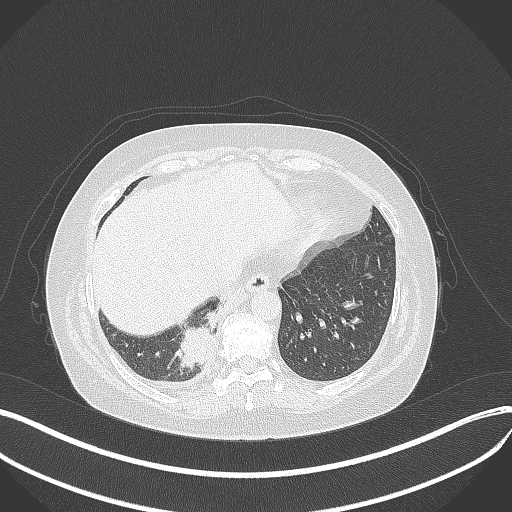
Chest CT, one axial slice; slice 92 of 381 in the series (ordered by position); reconstruction kernel B70f; lung window (W 1500 / L -600 HU); 1 mm slice thickness; 512 × 512 image matrix, field of view 400 × 400 mm. Patient: female, 56 years. Case-level facts recorded for this patient, not image findings: clinical TNM (as recorded): T2b N1 M0; histopathological grade: G3.
Outlined on this slice (bounding box drawn by a radiologist):
- lung tumour (recorded histology: small cell carcinoma): box from (x=171, y=312) to (x=227, y=372) px